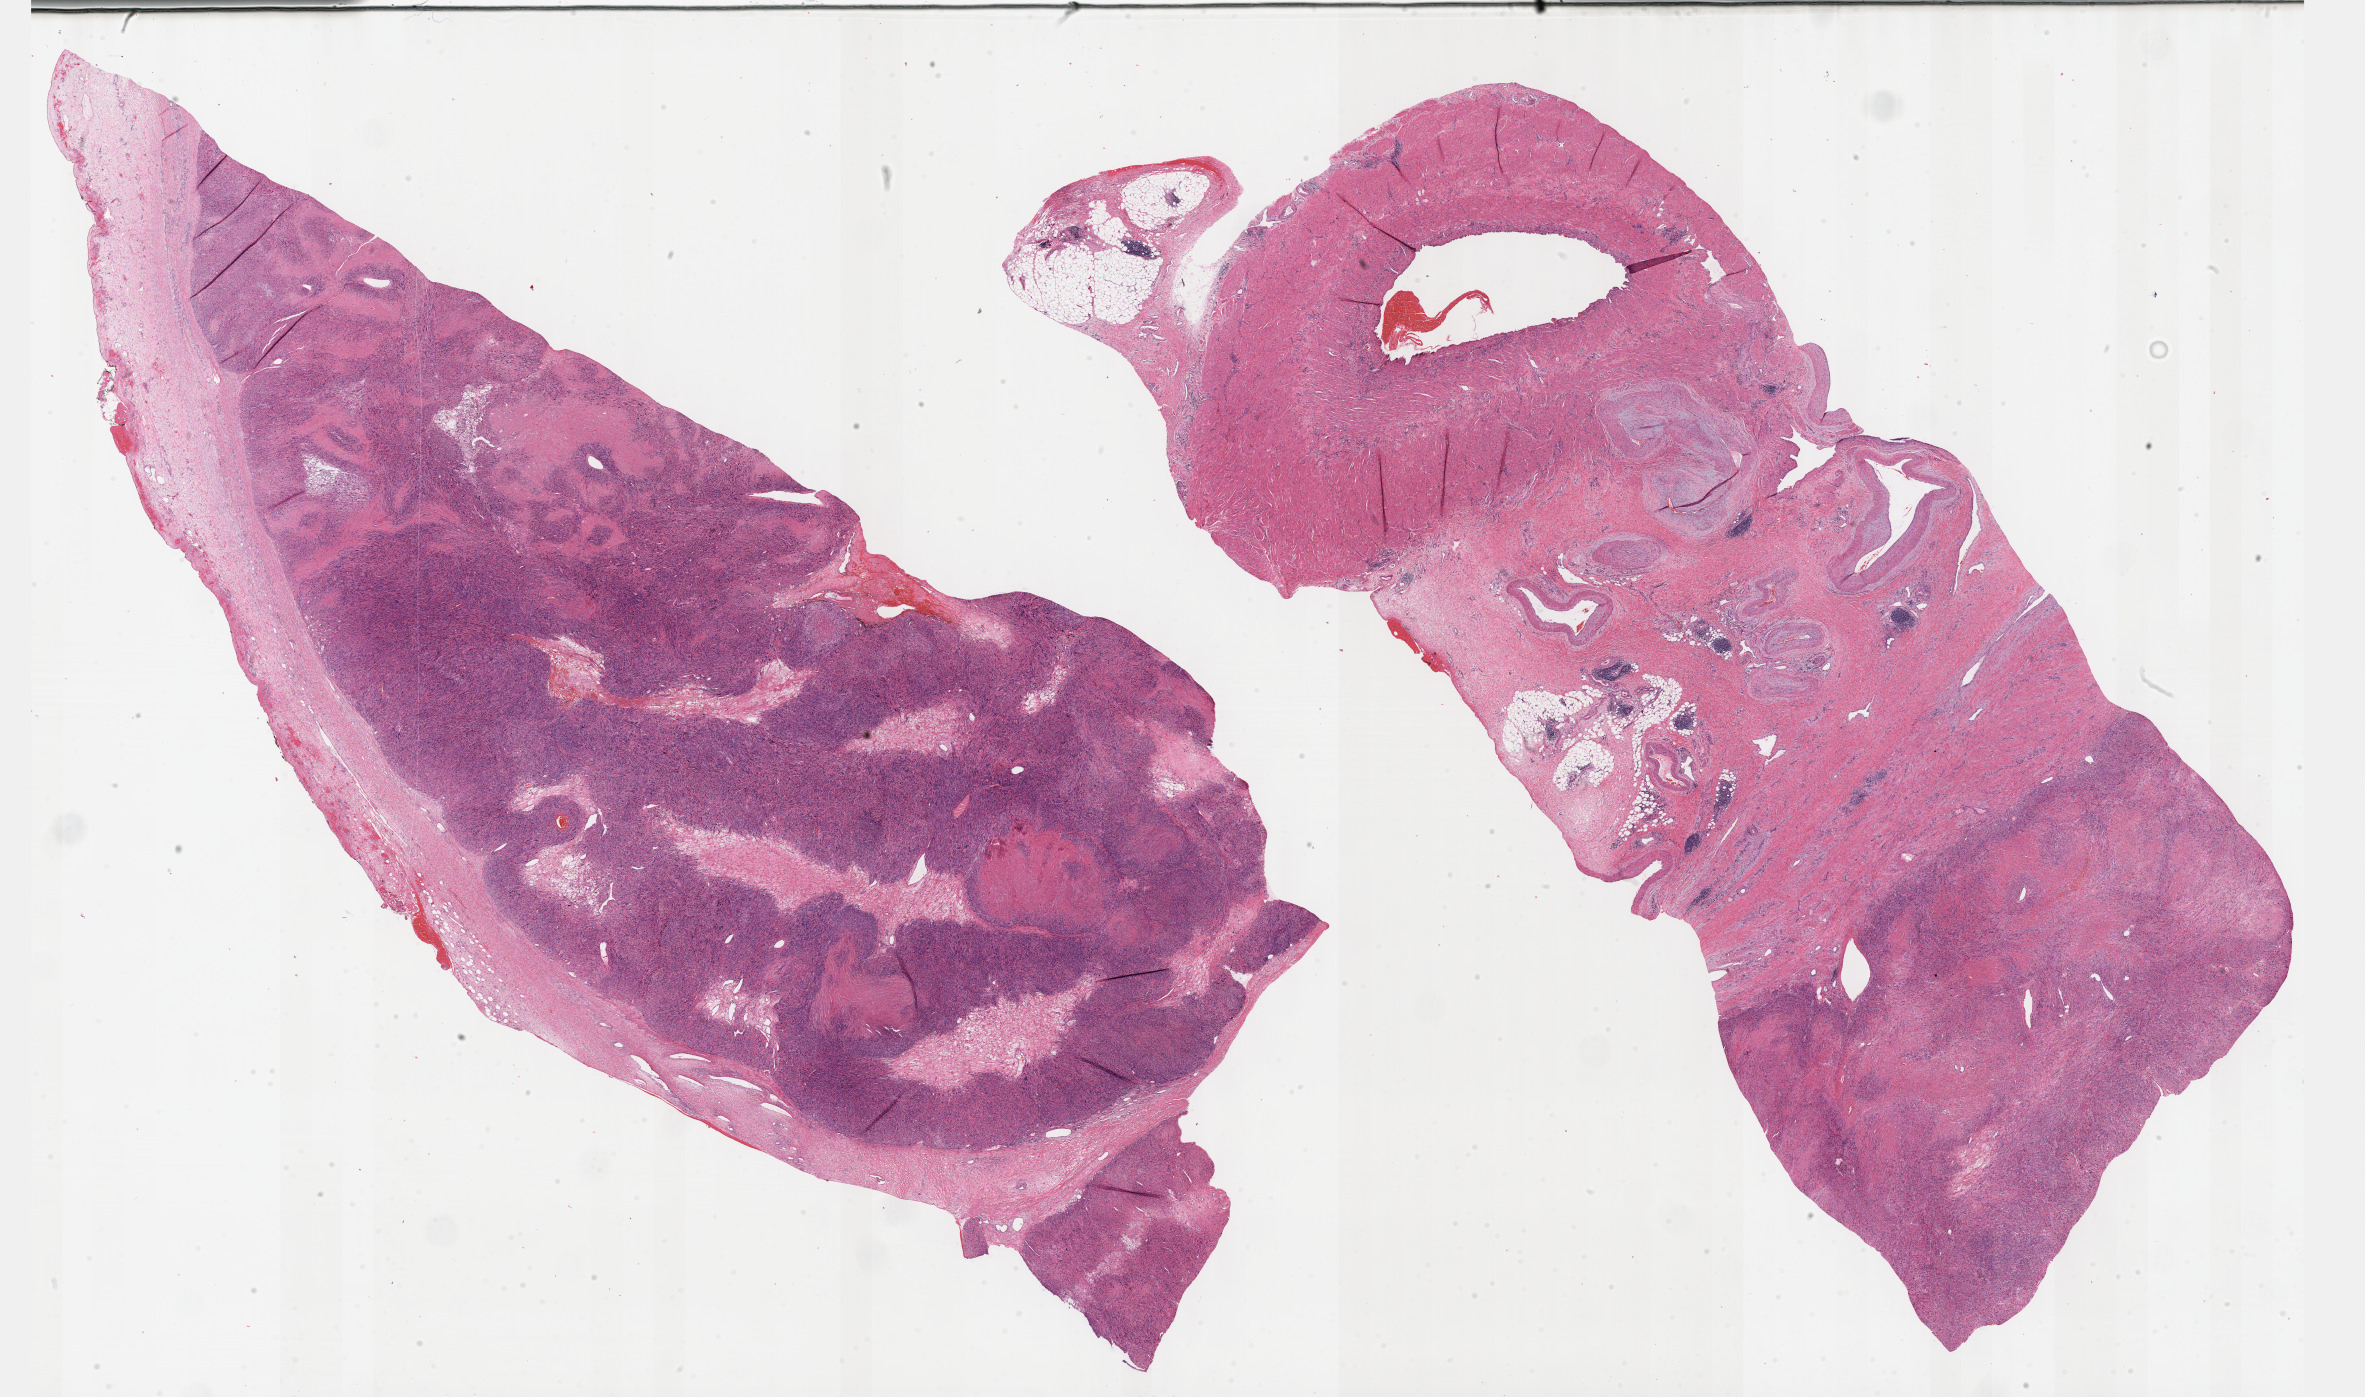
H&E whole-slide image — low-resolution overview of the scanned area, about 38.2 x 22.6 mm; formalin-fixed paraffin-embedded (FFPE) diagnostic section; retroperitoneum and peritoneum, primary tumour sample. Female, age 63 years at initial diagnosis.
Pathologic diagnosis: Leiomyosarcoma, NOS (retroperitoneum).